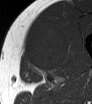
MRI of an extremity soft-tissue mass, one axial slice. MR volume resampled by the dataset authors to the PET/CT grid (not the native acquisition matrix). 3.27 mm slice thickness. 92 × 104 image matrix. Male patient. Case-level facts recorded for this patient, not image findings: histological type: mixoid liposarcoma; grade: low; site of the primary tumour: left thigh.
Outlined on this slice (expert contour drawn on MRI and transferred to this co-registered scan by the dataset authors):
- gross tumour volume (mass): bounding box [x1, y1, x2, y2] px = [23, 24, 68, 71]